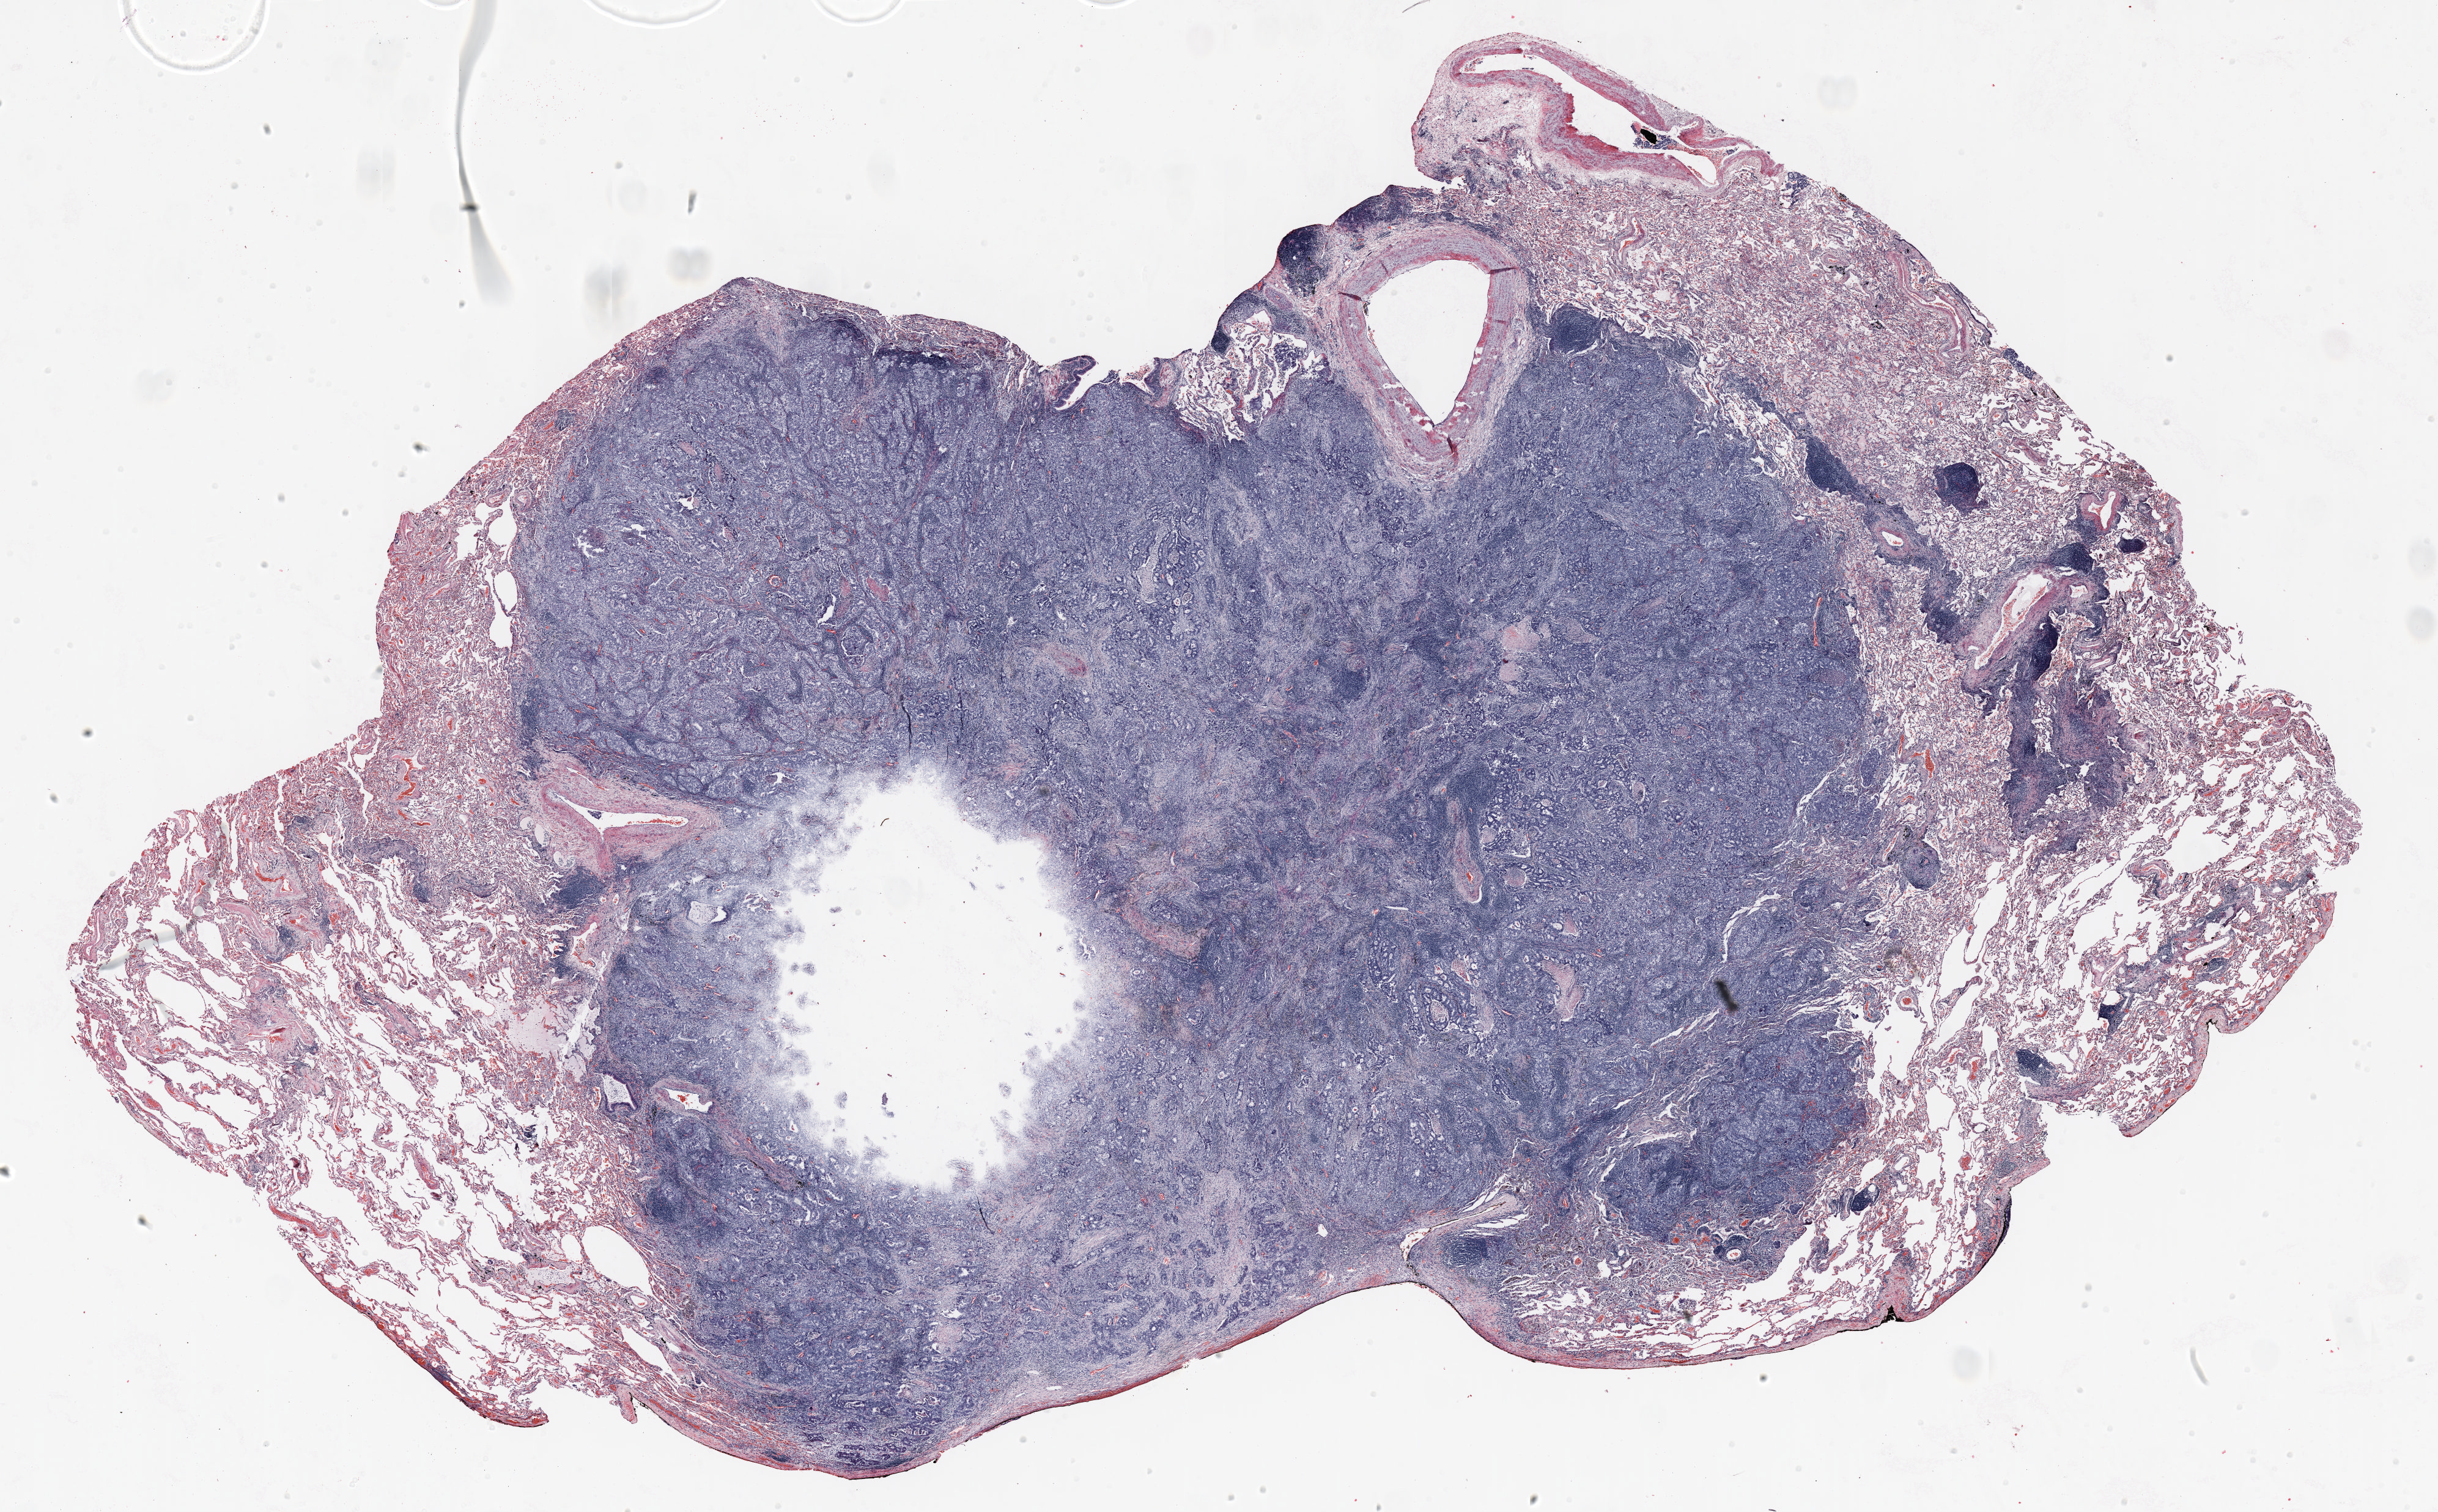
Hematoxylin and eosin (H&E) stained whole-slide image — whole scanned area (about 32.0 x 19.9 mm, from a 20x scan) shown as a low-resolution overview. Formalin-fixed paraffin-embedded (FFPE) section. Lung. Male, age 70 at enrolment. Grade: poorly differentiated (G3).
Stage (AJCC 6th edition): IIA. Participant's lung-cancer diagnosis: Adenocarcinoma, NOS. Primary tumour location (clinical record): right upper lobe. Tumour size (pathology): 23 mm.